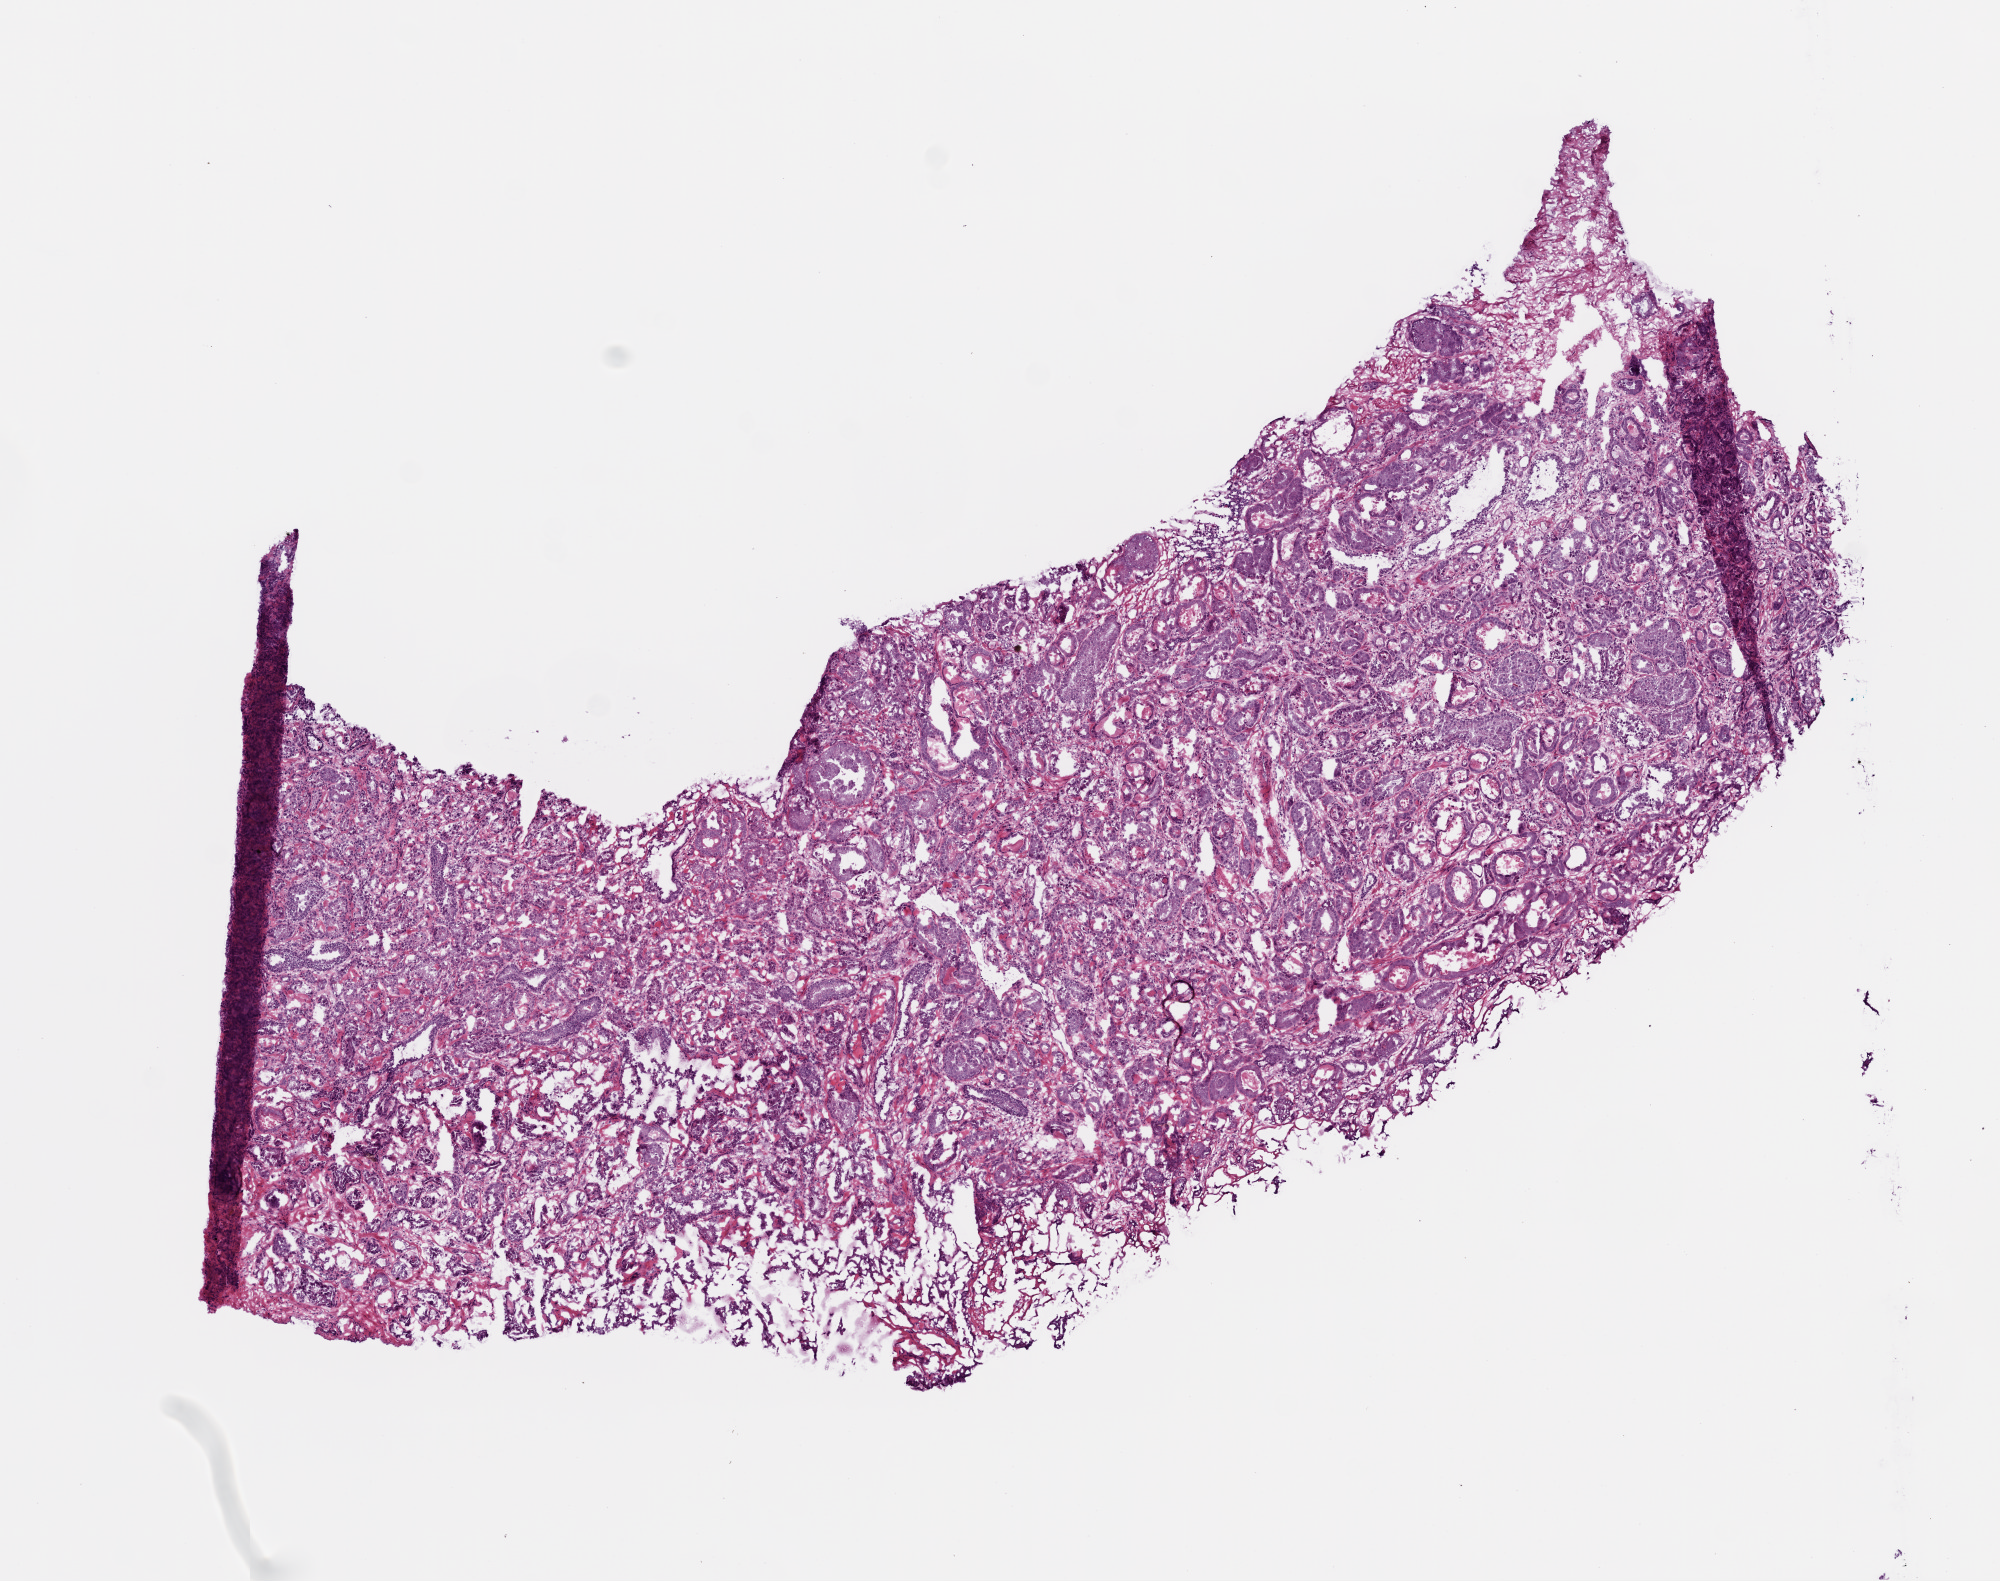
H&E whole-slide image, shown as a low-resolution overview of the whole scanned area (about 8.0 x 6.3 mm, acquisition: 20x scan), frozen section from the top of the tissue portion, primary tumour sample from the prostate. Male, age 55 years at initial diagnosis. Gleason score: 7 (4+3). Slide review estimates, as recorded: tumour cells 75%, tumour nuclei 80%, normal cells 15%, stromal cells 10%, necrosis 0%. Infiltration values recorded for this section: lymphocyte infiltration 0%, monocyte infiltration 0%, neutrophil infiltration 0%.
Histologic diagnosis: Acinar cell carcinoma (prostate gland). Lymph nodes positive (case pathology): 1 of 4 examined.